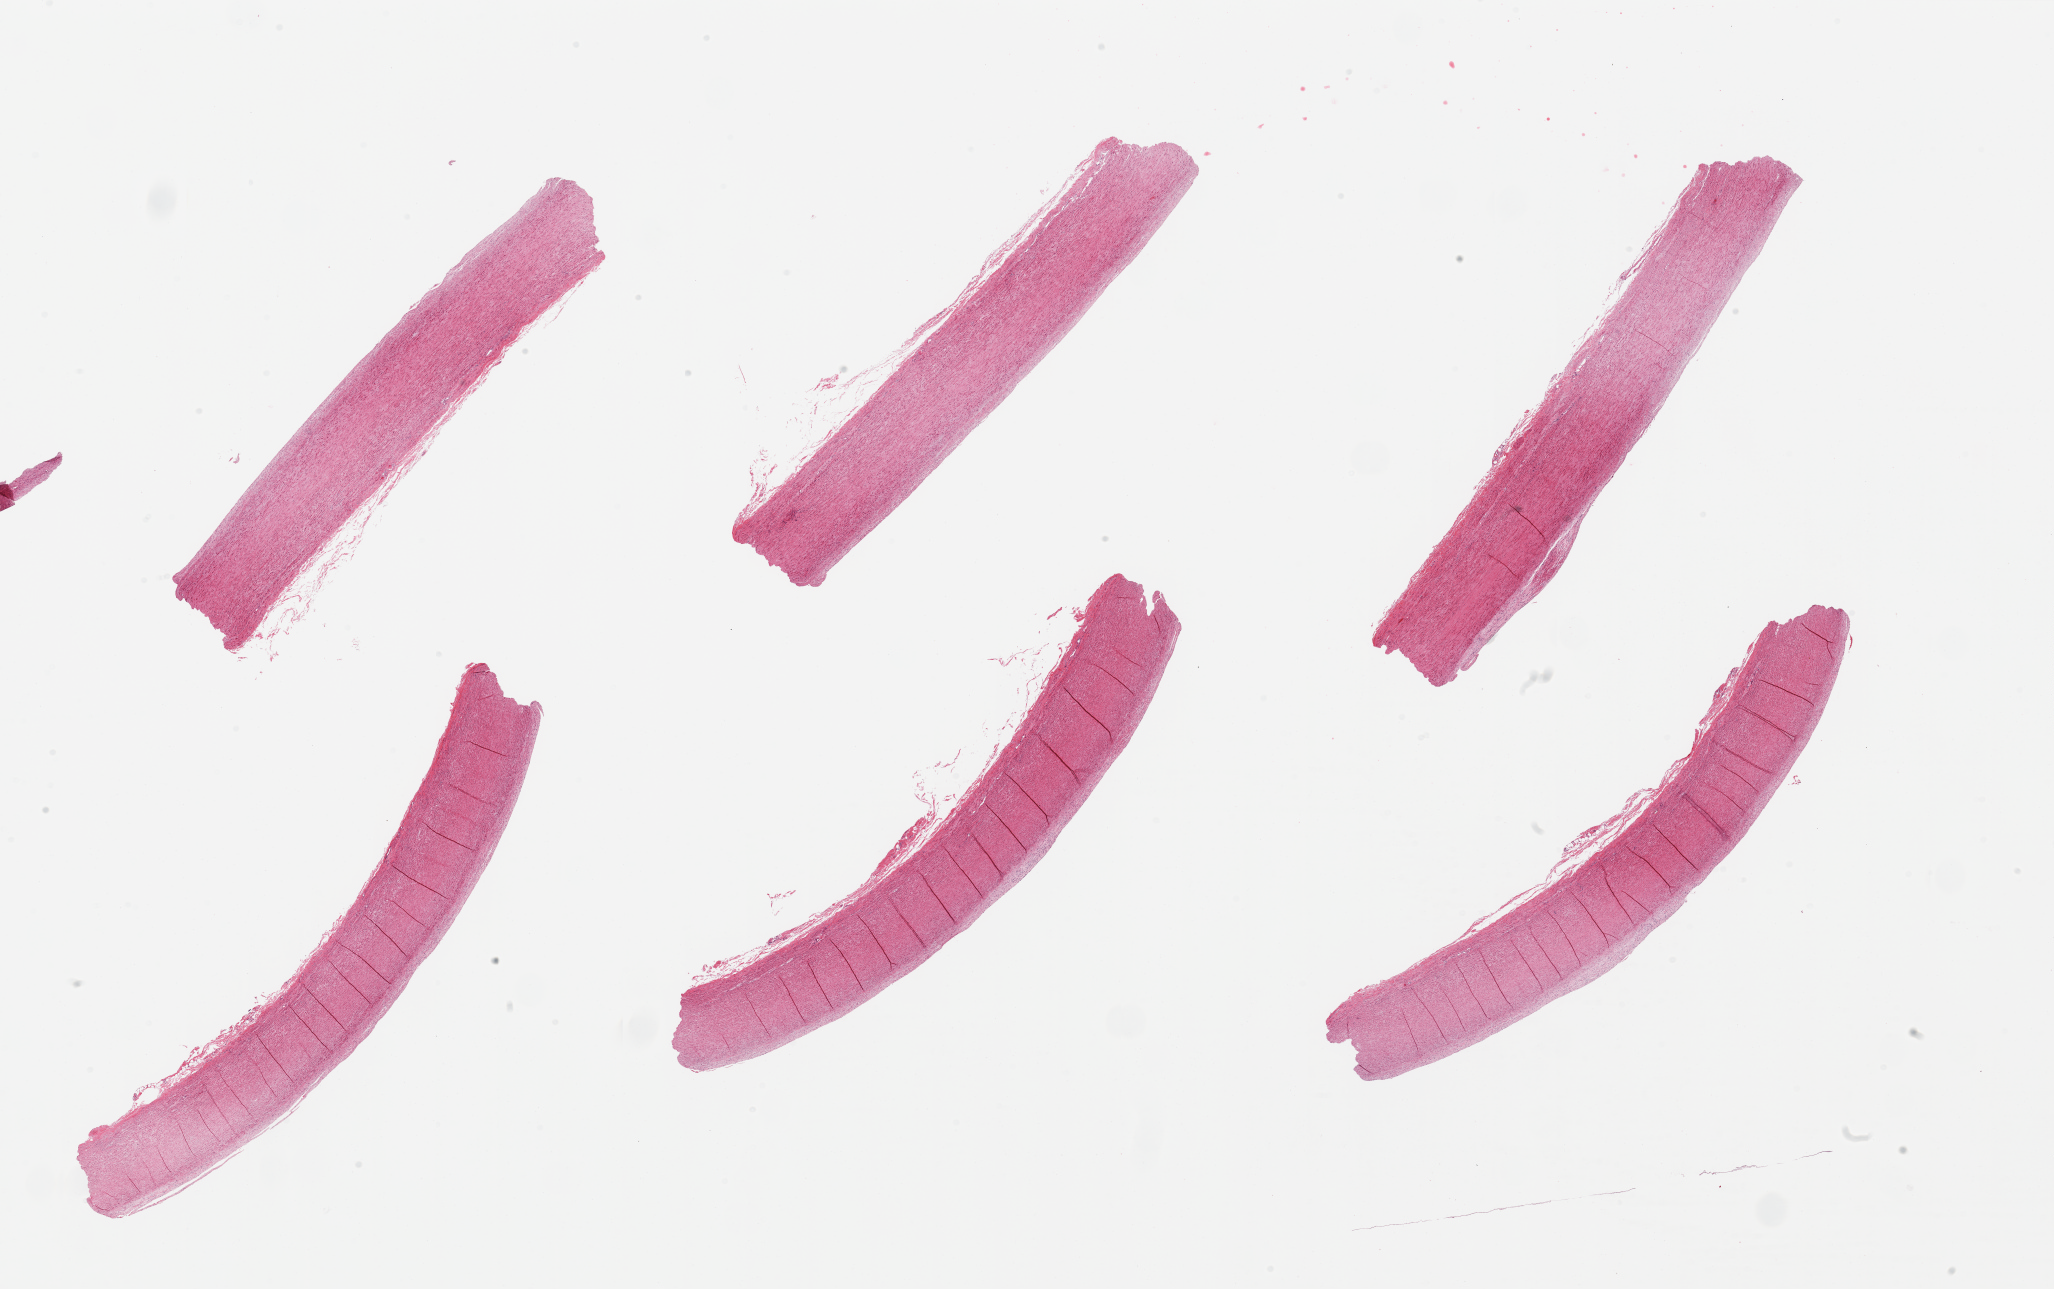
Whole-slide image, hematoxylin and eosin (H&E) stain — a low-resolution overview of the entire scanned area, about 32.5 x 20.4 mm; PAXgene-fixed, paraffin-embedded tissue; target tissue: aorta; tissue donor sample. Donor sex: male.
* reviewer comment on this tissue sample: 6 pieces, atherosis up to ~0.3mm